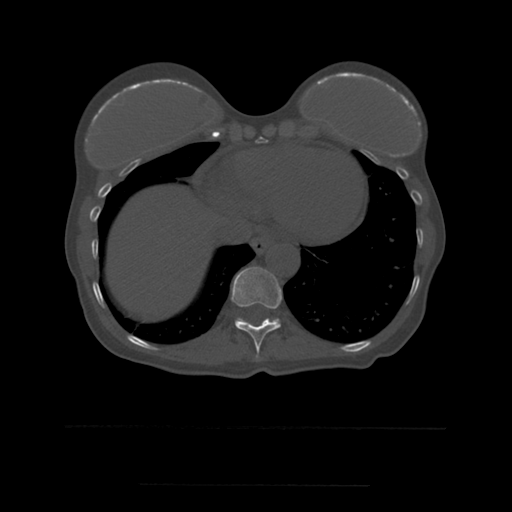
CT including the spine, one axial slice. Position 297 of 544 along the scan axis. Bone window (W 1800 / L 400 HU). 1.25 mm slice thickness. 512 × 512 image matrix. Patient age 58 years. Case-level facts recorded for this patient, not image findings: primary cancer: lung.
Structures marked on this image (semi-automatic segmentation, software-assisted and operator-edited):
- T10 vertebra: box from (x=231, y=267) to (x=282, y=358) px
- T11 vertebra: (x=236, y=318)–(x=280, y=323)